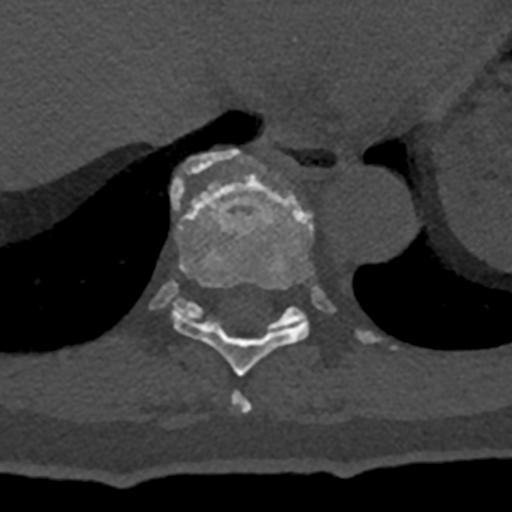
CT including the spine, one axial slice; position 640 of 797 along the scan axis; reconstruction kernel Br40s/3; 120 kVp; bone window (W 1800 / L 400 HU); 0.5 mm slice thickness; 512 × 512 image matrix, field of view 160 × 160 mm. Patient: male, 74 years. From the clinical record (not read from this slice): primary cancer: renal.
Structures marked on this image (semi-automatic segmentation, software-assisted and operator-edited):
- T10 vertebra: box from (x=150, y=149) to (x=396, y=348) px
- T8 vertebra: (x=231, y=390)–(x=252, y=413)
- T9 vertebra: (x=171, y=178)–(x=314, y=376)